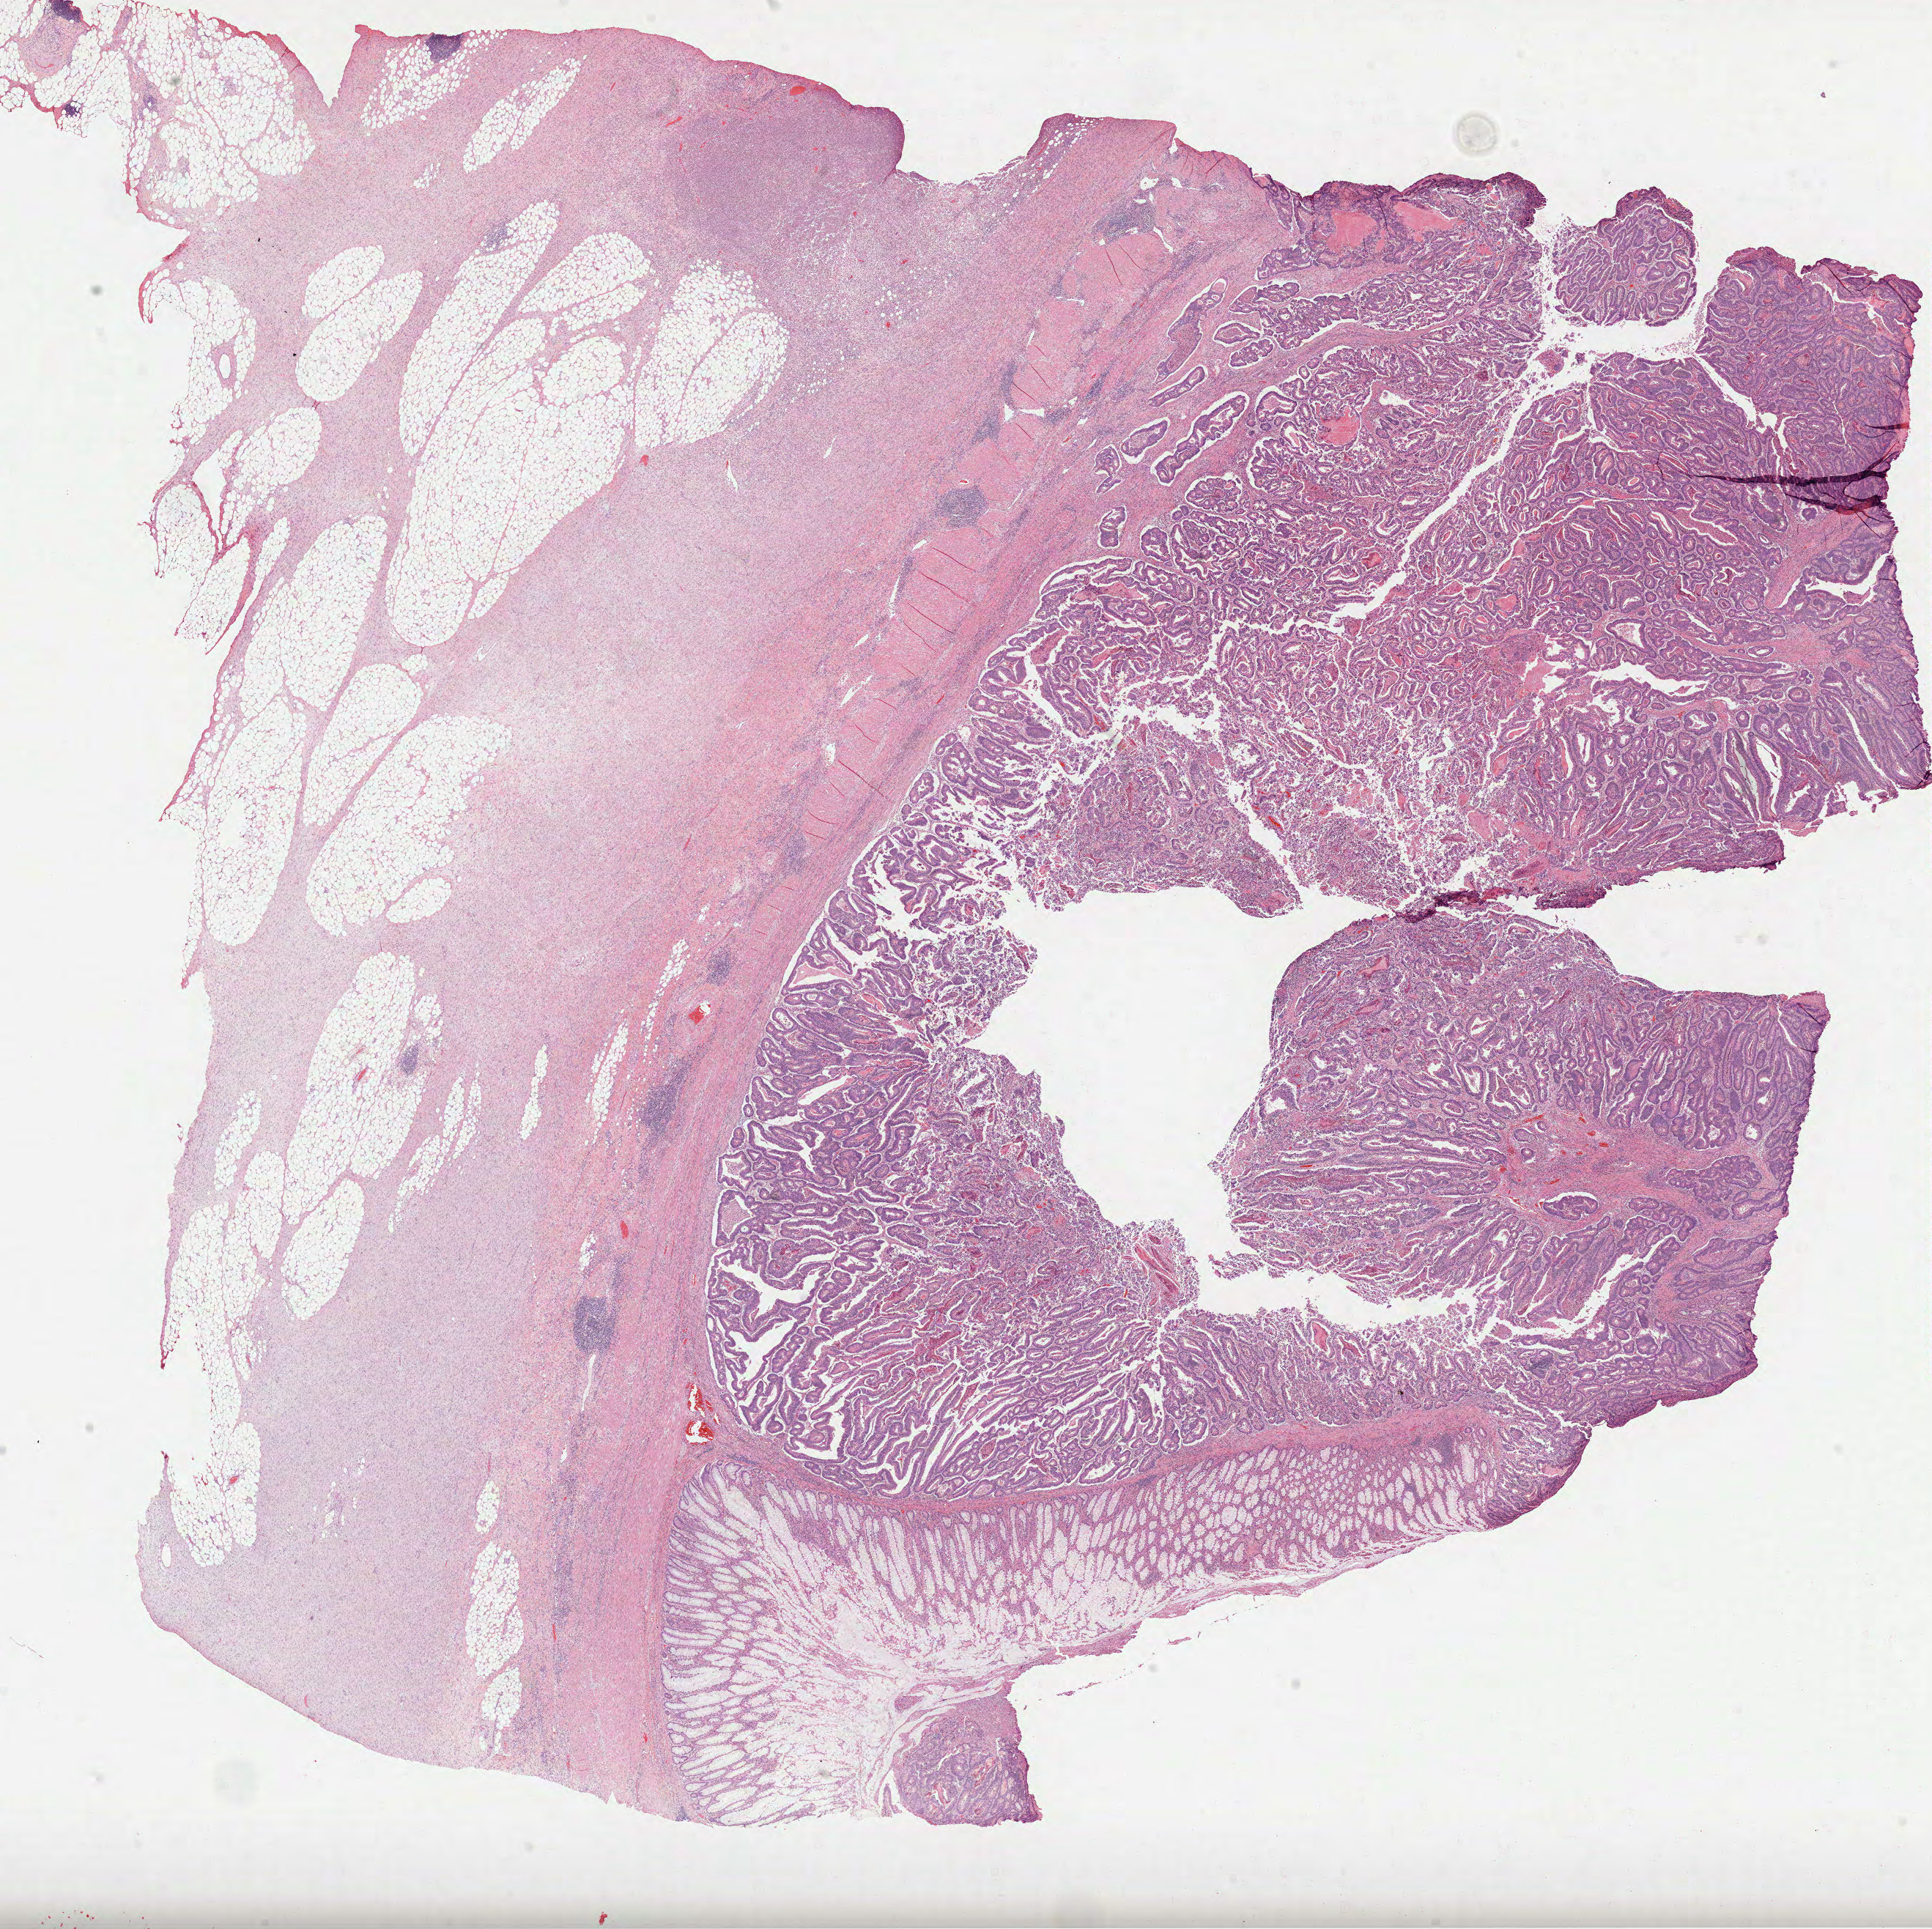
Digitized Hematoxylin and eosin (H&E) stained tissue section (whole slide), a low-resolution overview of the entire scanned area, about 21.3 x 21.2 mm. Formalin-fixed paraffin-embedded (FFPE) diagnostic section. Colon, primary tumour sample. Male, age 66 years at initial diagnosis.
* TNM: T3 N1 M1
* histologic diagnosis: Adenocarcinoma, NOS (descending colon)
* AJCC pathologic stage: IV (6th edition)